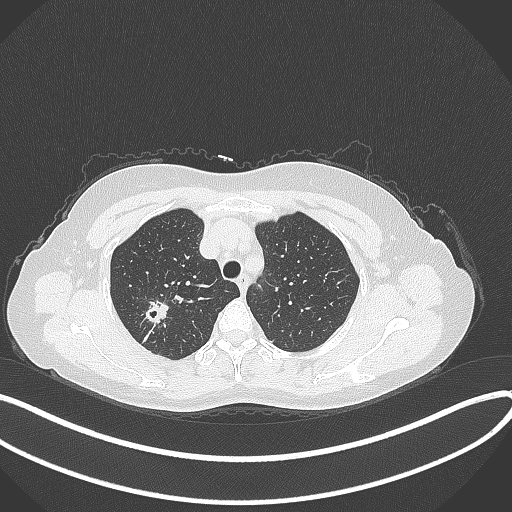
Chest CT, one axial slice. Position 290 of 337 along the scan axis. Reconstruction kernel B70f. 120 kVp. Lung window (W 1500 / L -600 HU). 1 mm slice thickness. 512 × 512 image matrix. Female patient, age 50 years. Case-level facts recorded for this patient, not image findings: clinical TNM (as recorded): T1c N0 M0.
Outlined on this slice (rectangle marked by the reading radiologist):
- lung tumour (recorded histology: adenocarcinoma): bounding box <142,300,173,326> (left, top, right, bottom; pixels)